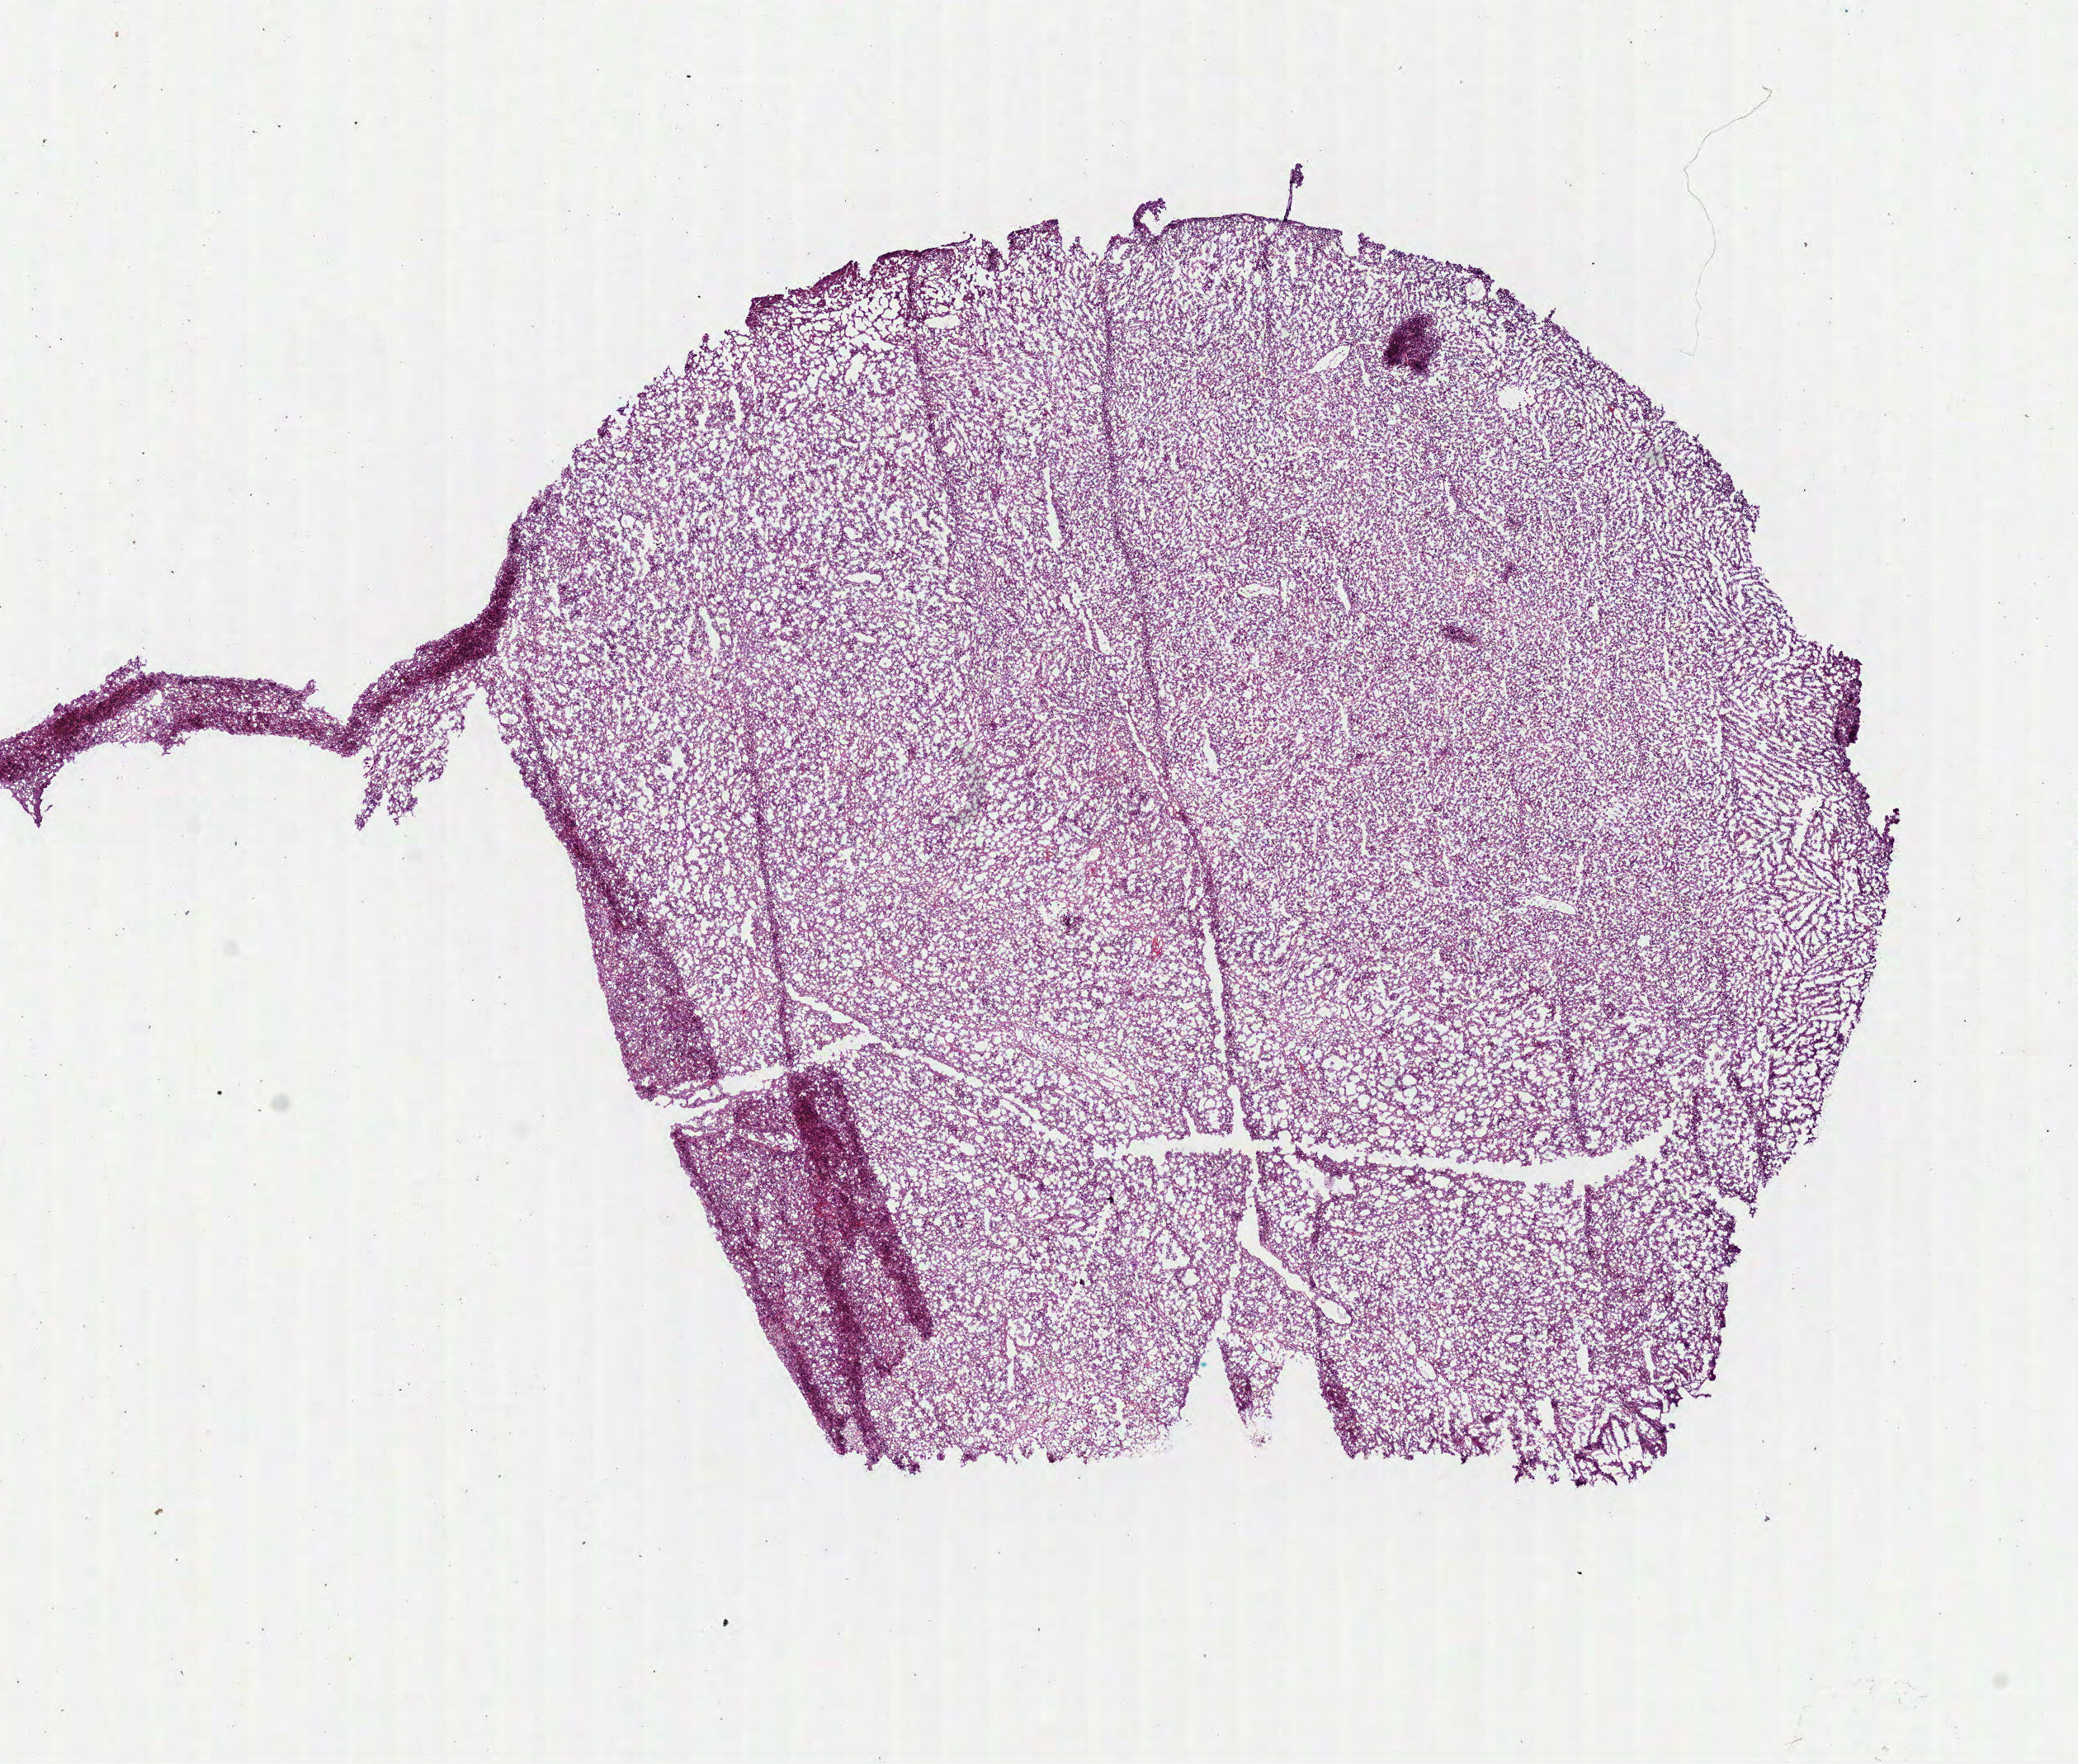
Digitized H&E-stained tissue section (whole slide) — low-resolution overview of the scanned area, about 10.2 x 8.6 mm (slide scanned at 40x), frozen section from the bottom of the tissue portion, primary tumour sample from the lymphoid tissue. Male, age 69 years at initial diagnosis. Slide review estimates, as recorded: tumour cells 95%, tumour nuclei 75%, normal cells 0%, stromal cells 5%, necrosis 0%.
Histologic diagnosis: Diffuse large B-cell lymphoma, NOS.